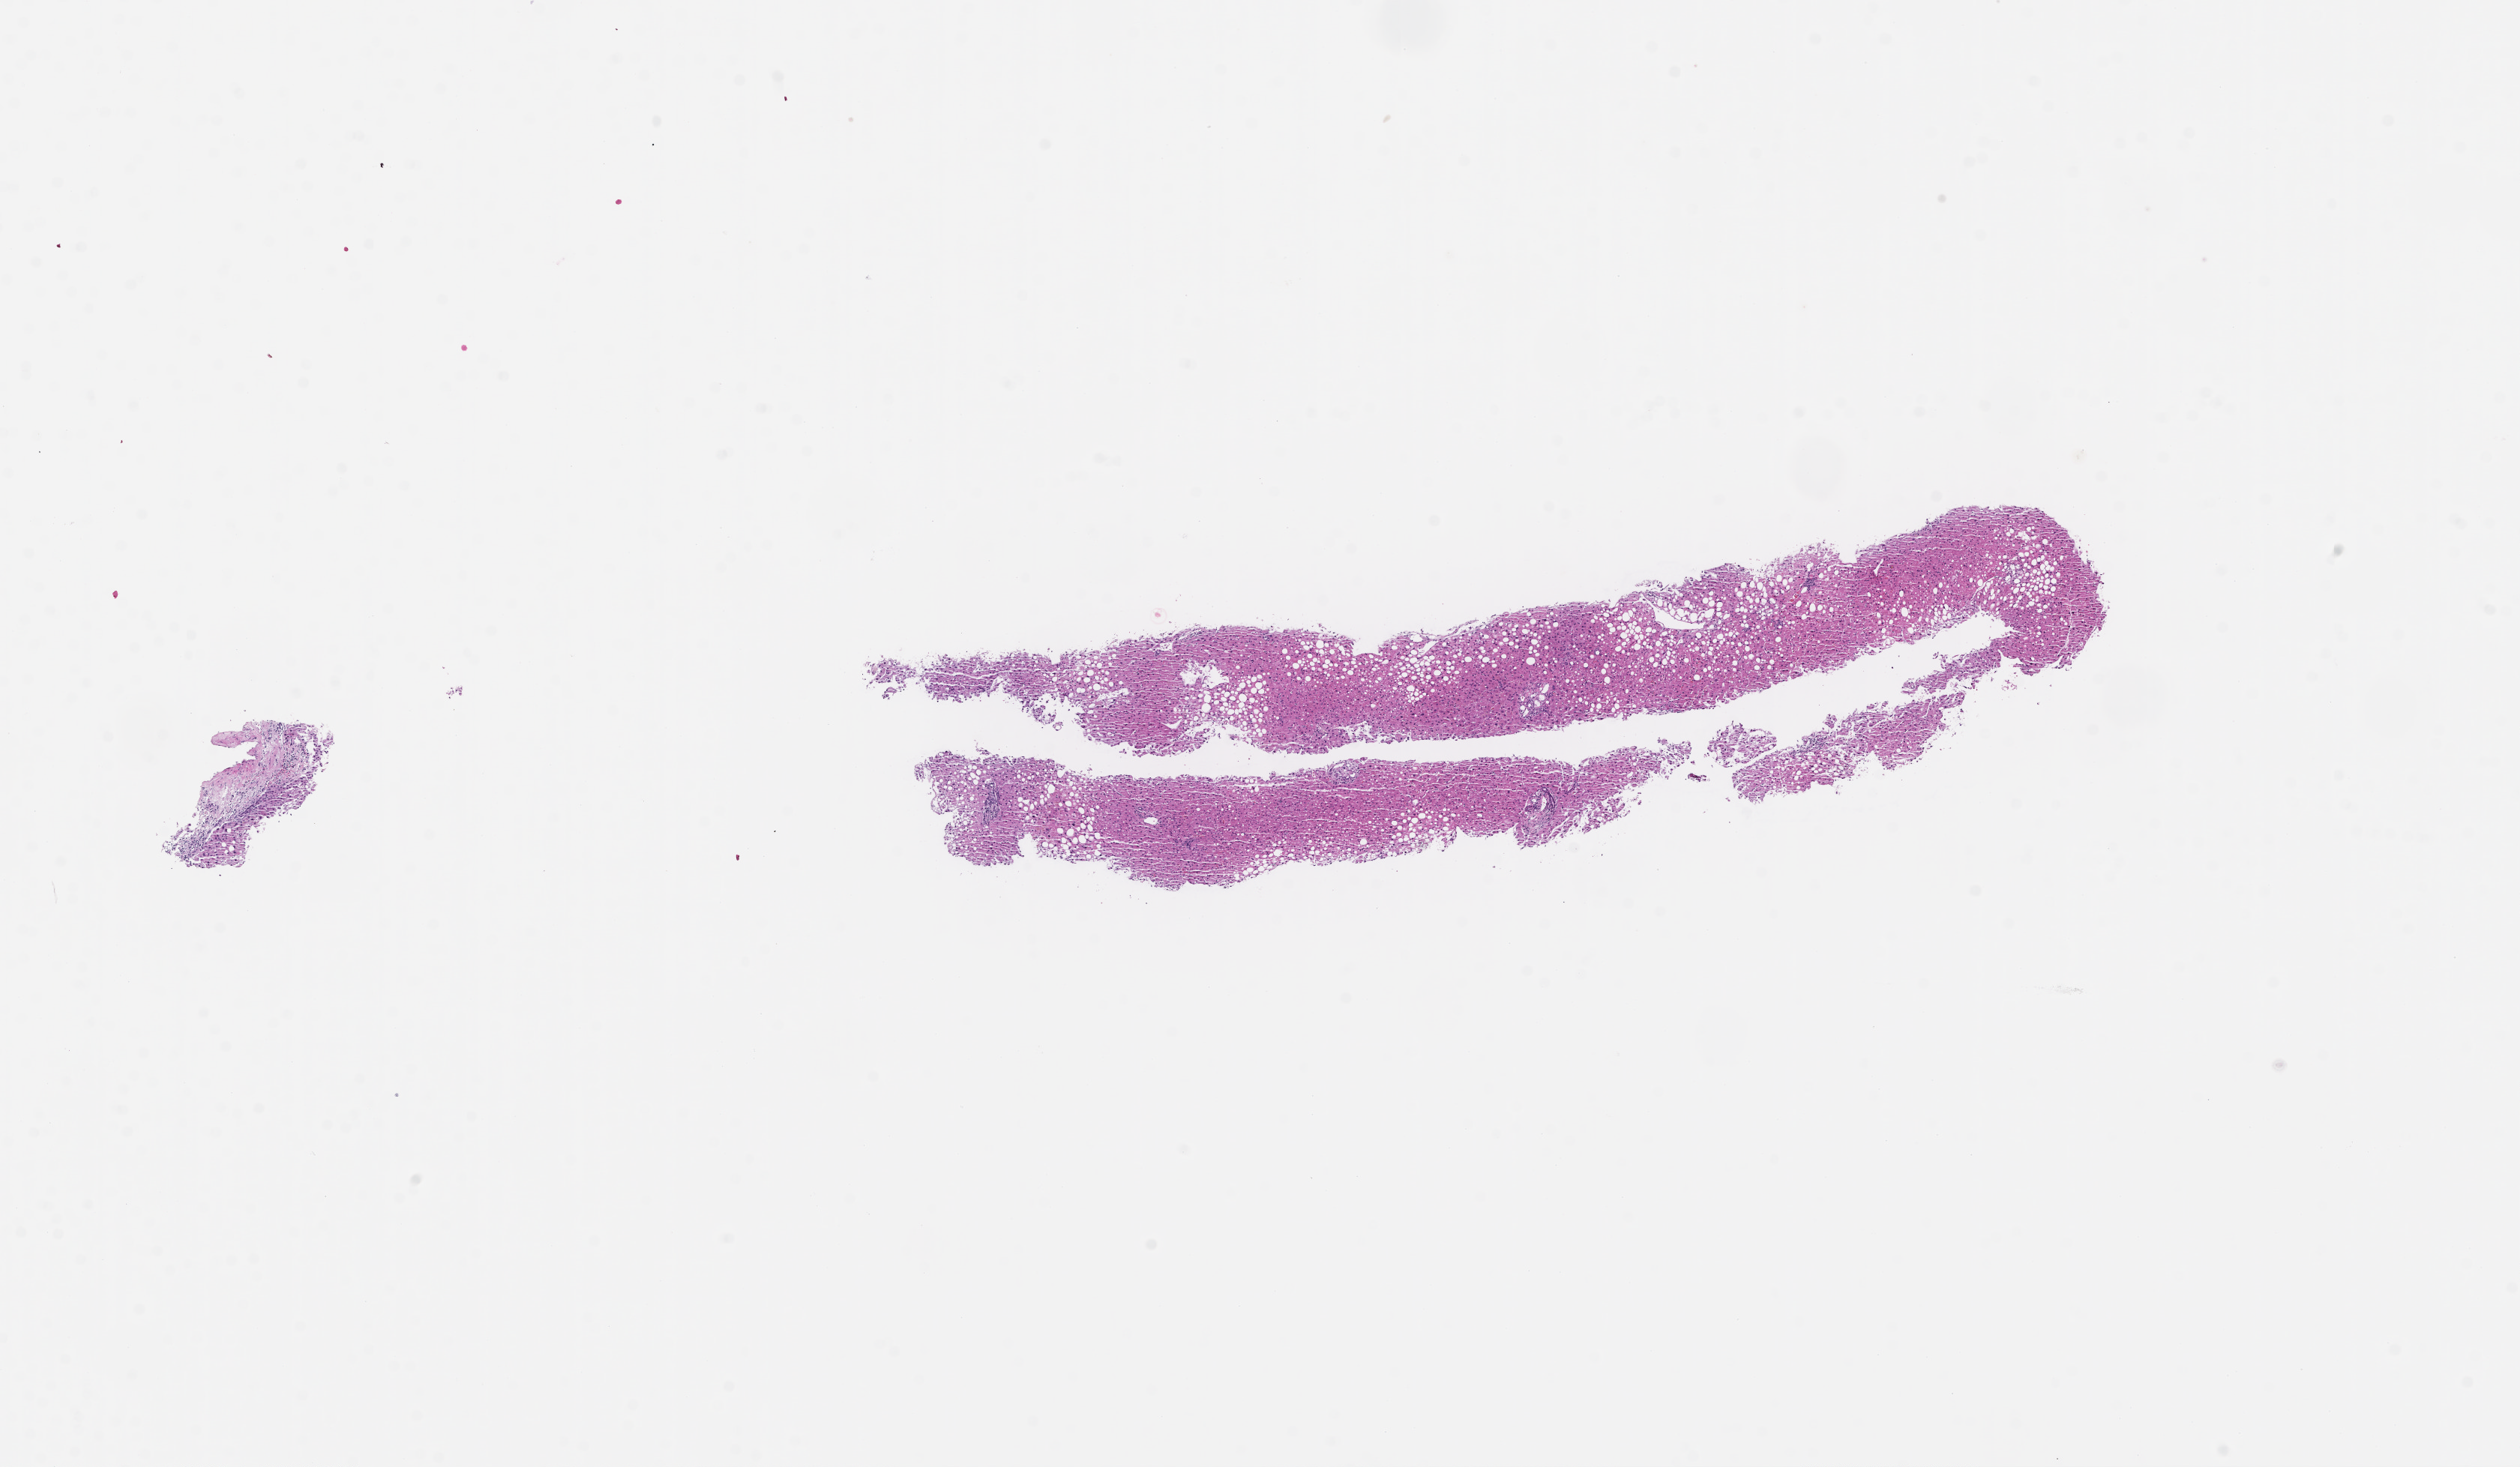
Whole-slide image, haematoxylin and eosin stain — a low-resolution overview of the entire scanned area, about 13.6 x 7.9 mm. FFPE section. Specimen time point: collected at baseline (before treatment). Male patient.
• this section: metastatic tumor tissue
• primary diagnosis of the patient: Melanoma